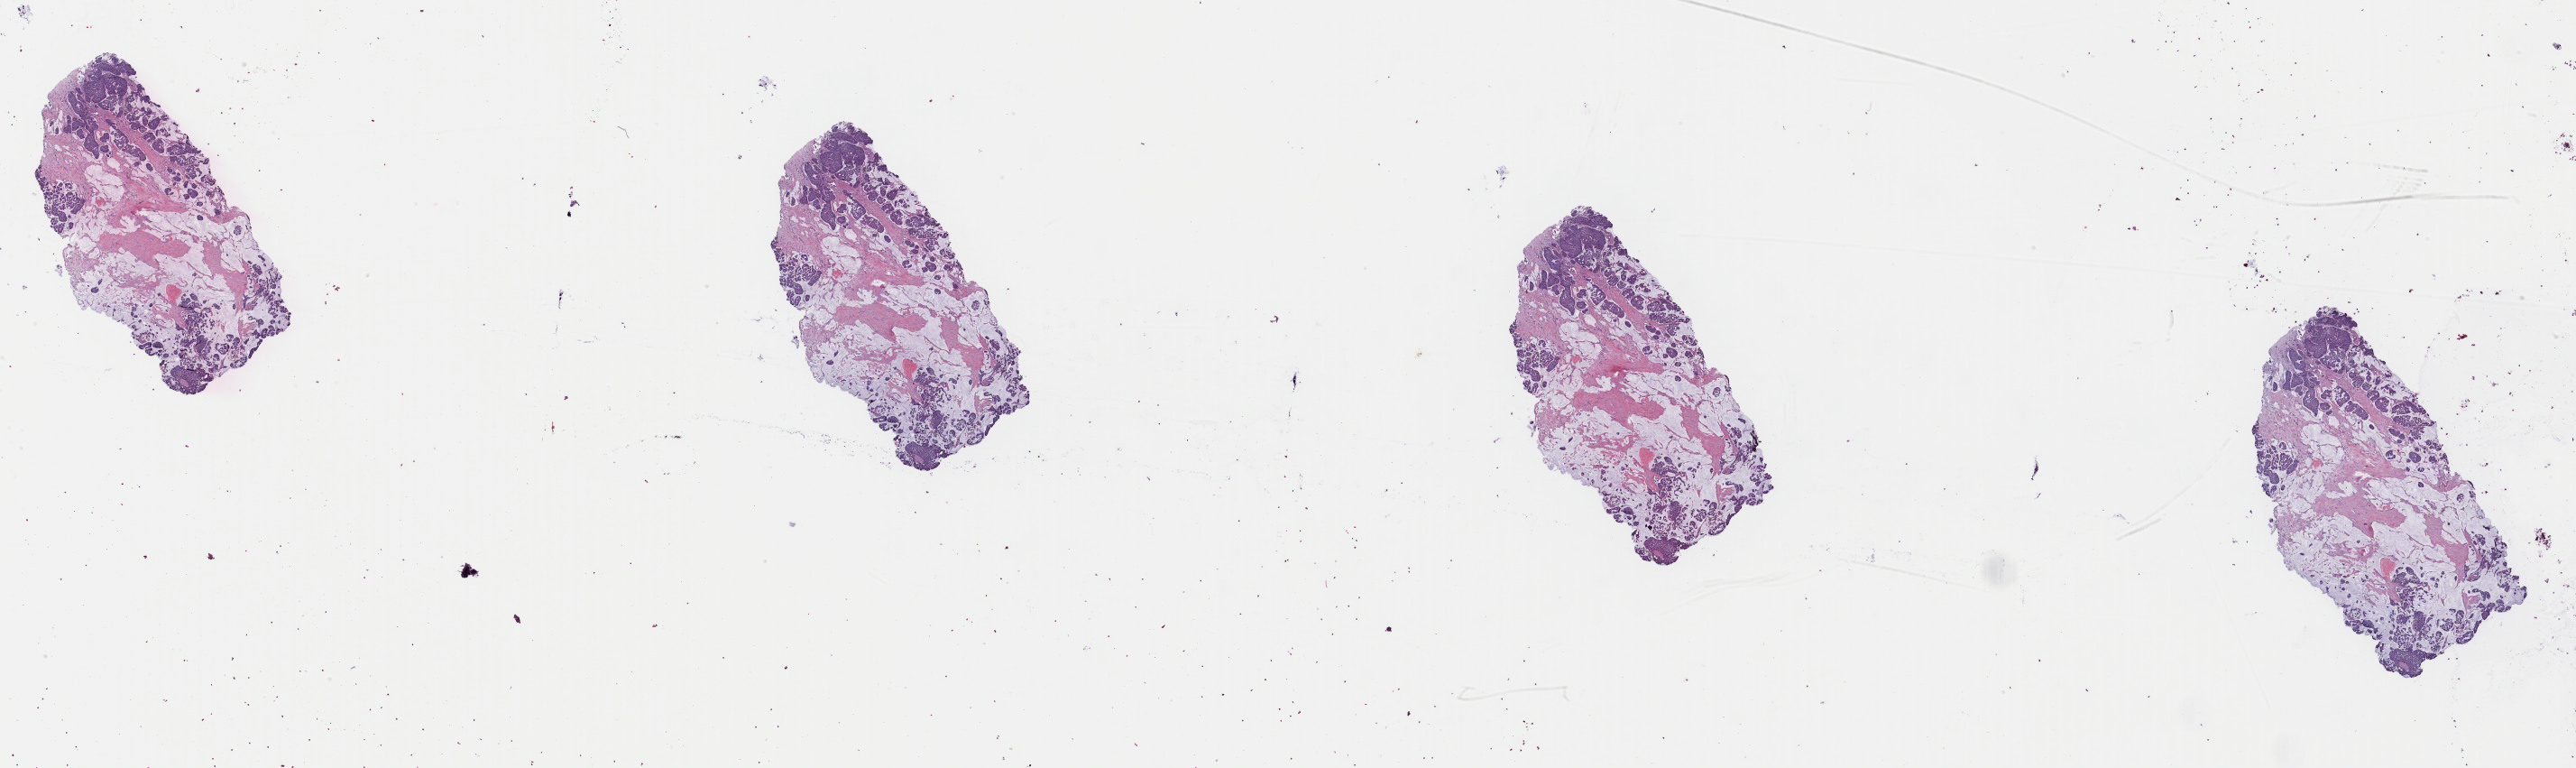
Whole-slide histology image, H&E-stained, shown as a low-resolution overview of the whole scanned area (about 45.1 x 13.4 mm), formalin-fixed paraffin-embedded (FFPE) diagnostic section, sample: primary tumour, breast. Female patient; age at initial diagnosis 79 years.
AJCC pathologic stage: IIA (7th edition). Histologic diagnosis: Mucinous adenocarcinoma. Lymph nodes positive (case pathology): 0 of 2 examined. Laterality: left.